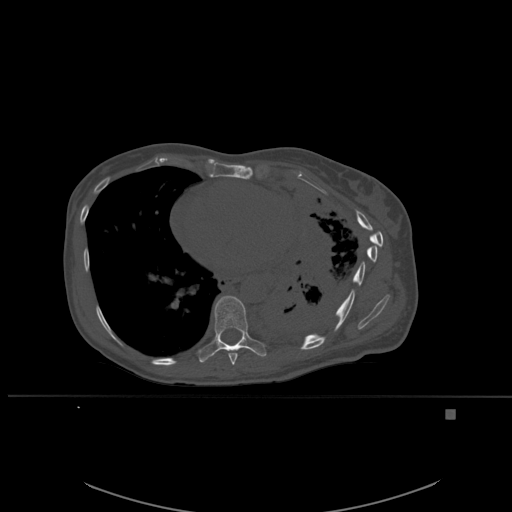
CT including the spine, one axial slice; slice 337 of 537 in the series (ordered by position); bone window (W 1800 / L 400 HU); 1.5 mm slice thickness; 512 × 512 image matrix, field of view 440 × 440 mm. Patient: female, 45 years. From the clinical record (not read from this slice): primary cancer: lung.
Annotated regions visible in this slice (semi-automatic segmentation, software-assisted and operator-edited):
- T8 vertebra: bounding box [x1, y1, x2, y2] px = [228, 350, 238, 365]
- T9 vertebra: [198, 296, 267, 363]